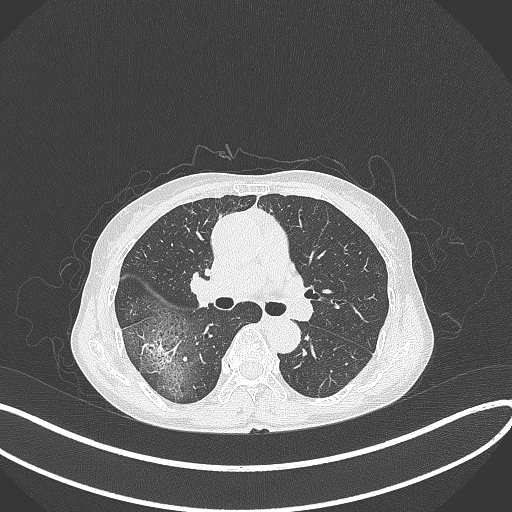
Chest CT, one axial slice. Position 236 of 371 along the scan axis. 120 kVp. Lung window (W 1500 / L -600 HU). 1 mm slice thickness. 512 × 512 image matrix, field of view 400 × 400 mm. Patient: female, 69 years. From the clinical record (not read from this slice): clinical TNM (as recorded): T1b N0 M0; histopathological grade: G2-3.
Structures marked on this image (rectangle marked by the reading radiologist):
- lung tumour (recorded histology: adenocarcinoma): box from (x=140, y=330) to (x=185, y=375) px